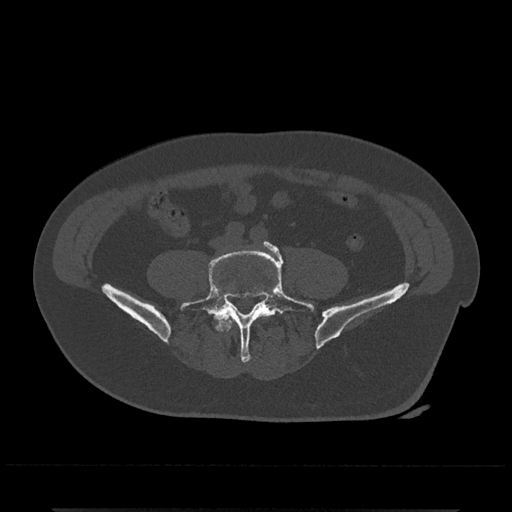
CT including the spine, one axial slice; slice 96 of 797 in the series (ordered by position); reconstruction kernel Br40s/3; bone window (W 1800 / L 400 HU); 0.5 mm slice thickness; 512 × 512 image matrix, field of view 393 × 393 mm. Male patient, age 67 years. Case-level facts recorded for this patient, not image findings: primary cancer: prostate.
Structures marked on this image (semi-automatic segmentation, software-assisted and operator-edited):
- L4 vertebra: bounding box [x1, y1, x2, y2] px = [220, 318, 233, 332]
- L5 vertebra: [180, 241, 314, 363]